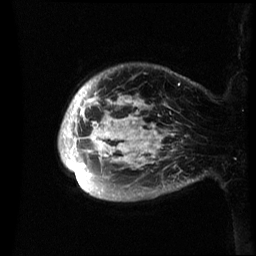
Breast MRI (dynamic contrast-enhanced), one sagittal slice. Position 5 of 60 along the scan axis. Dynamic contrast-enhanced series, image 2 of 3 at this slice position (ordered by acquisition). 1.5 T. TE 4.2 ms, TR 8.4 ms. 2.4 mm slice thickness. 256 × 256 image matrix, field of view 230 × 230 mm. Patient: female, 48 years.
Annotated regions visible in this slice (semi-automatic segmentation, software-assisted and operator-edited):
- analysis volume of interest (the breast-tissue region the enhancement analysis was run in; not a lesion): bounding box <58,66,195,201> (left, top, right, bottom; pixels)
- tumour enhancement mask (voxels above the 70 % enhancement threshold inside the analysis volume of interest): <60,84,180,183>